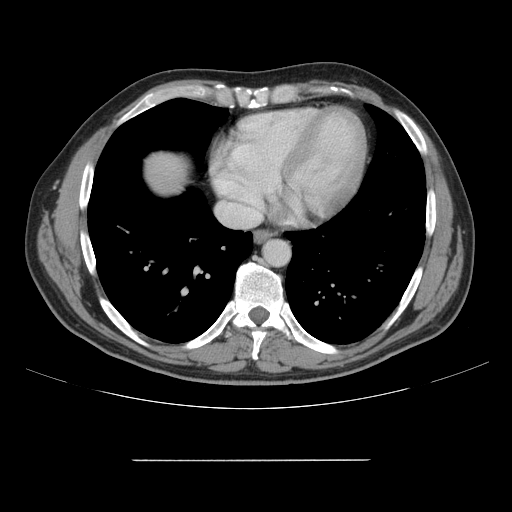
Contrast-enhanced abdominal CT, one axial slice; 120 kVp; intravenous contrast given; soft-tissue window (W 400 / L 40 HU); 512 × 512 image matrix, field of view 404 × 404 mm. Male patient, age 54 years. Case-level facts recorded for this patient, not image findings: diagnosis: colorectal cancer liver metastases, imaged before liver resection; multiple liver metastases: yes.
Annotated regions visible in this slice (outlined manually by an expert reader):
- hepatic veins: bounding box [x1, y1, x2, y2] px = [217, 202, 258, 224]
- liver: [145, 154, 186, 192]
- planned liver remnant (the part of the liver to remain after resection): [147, 154, 187, 193]